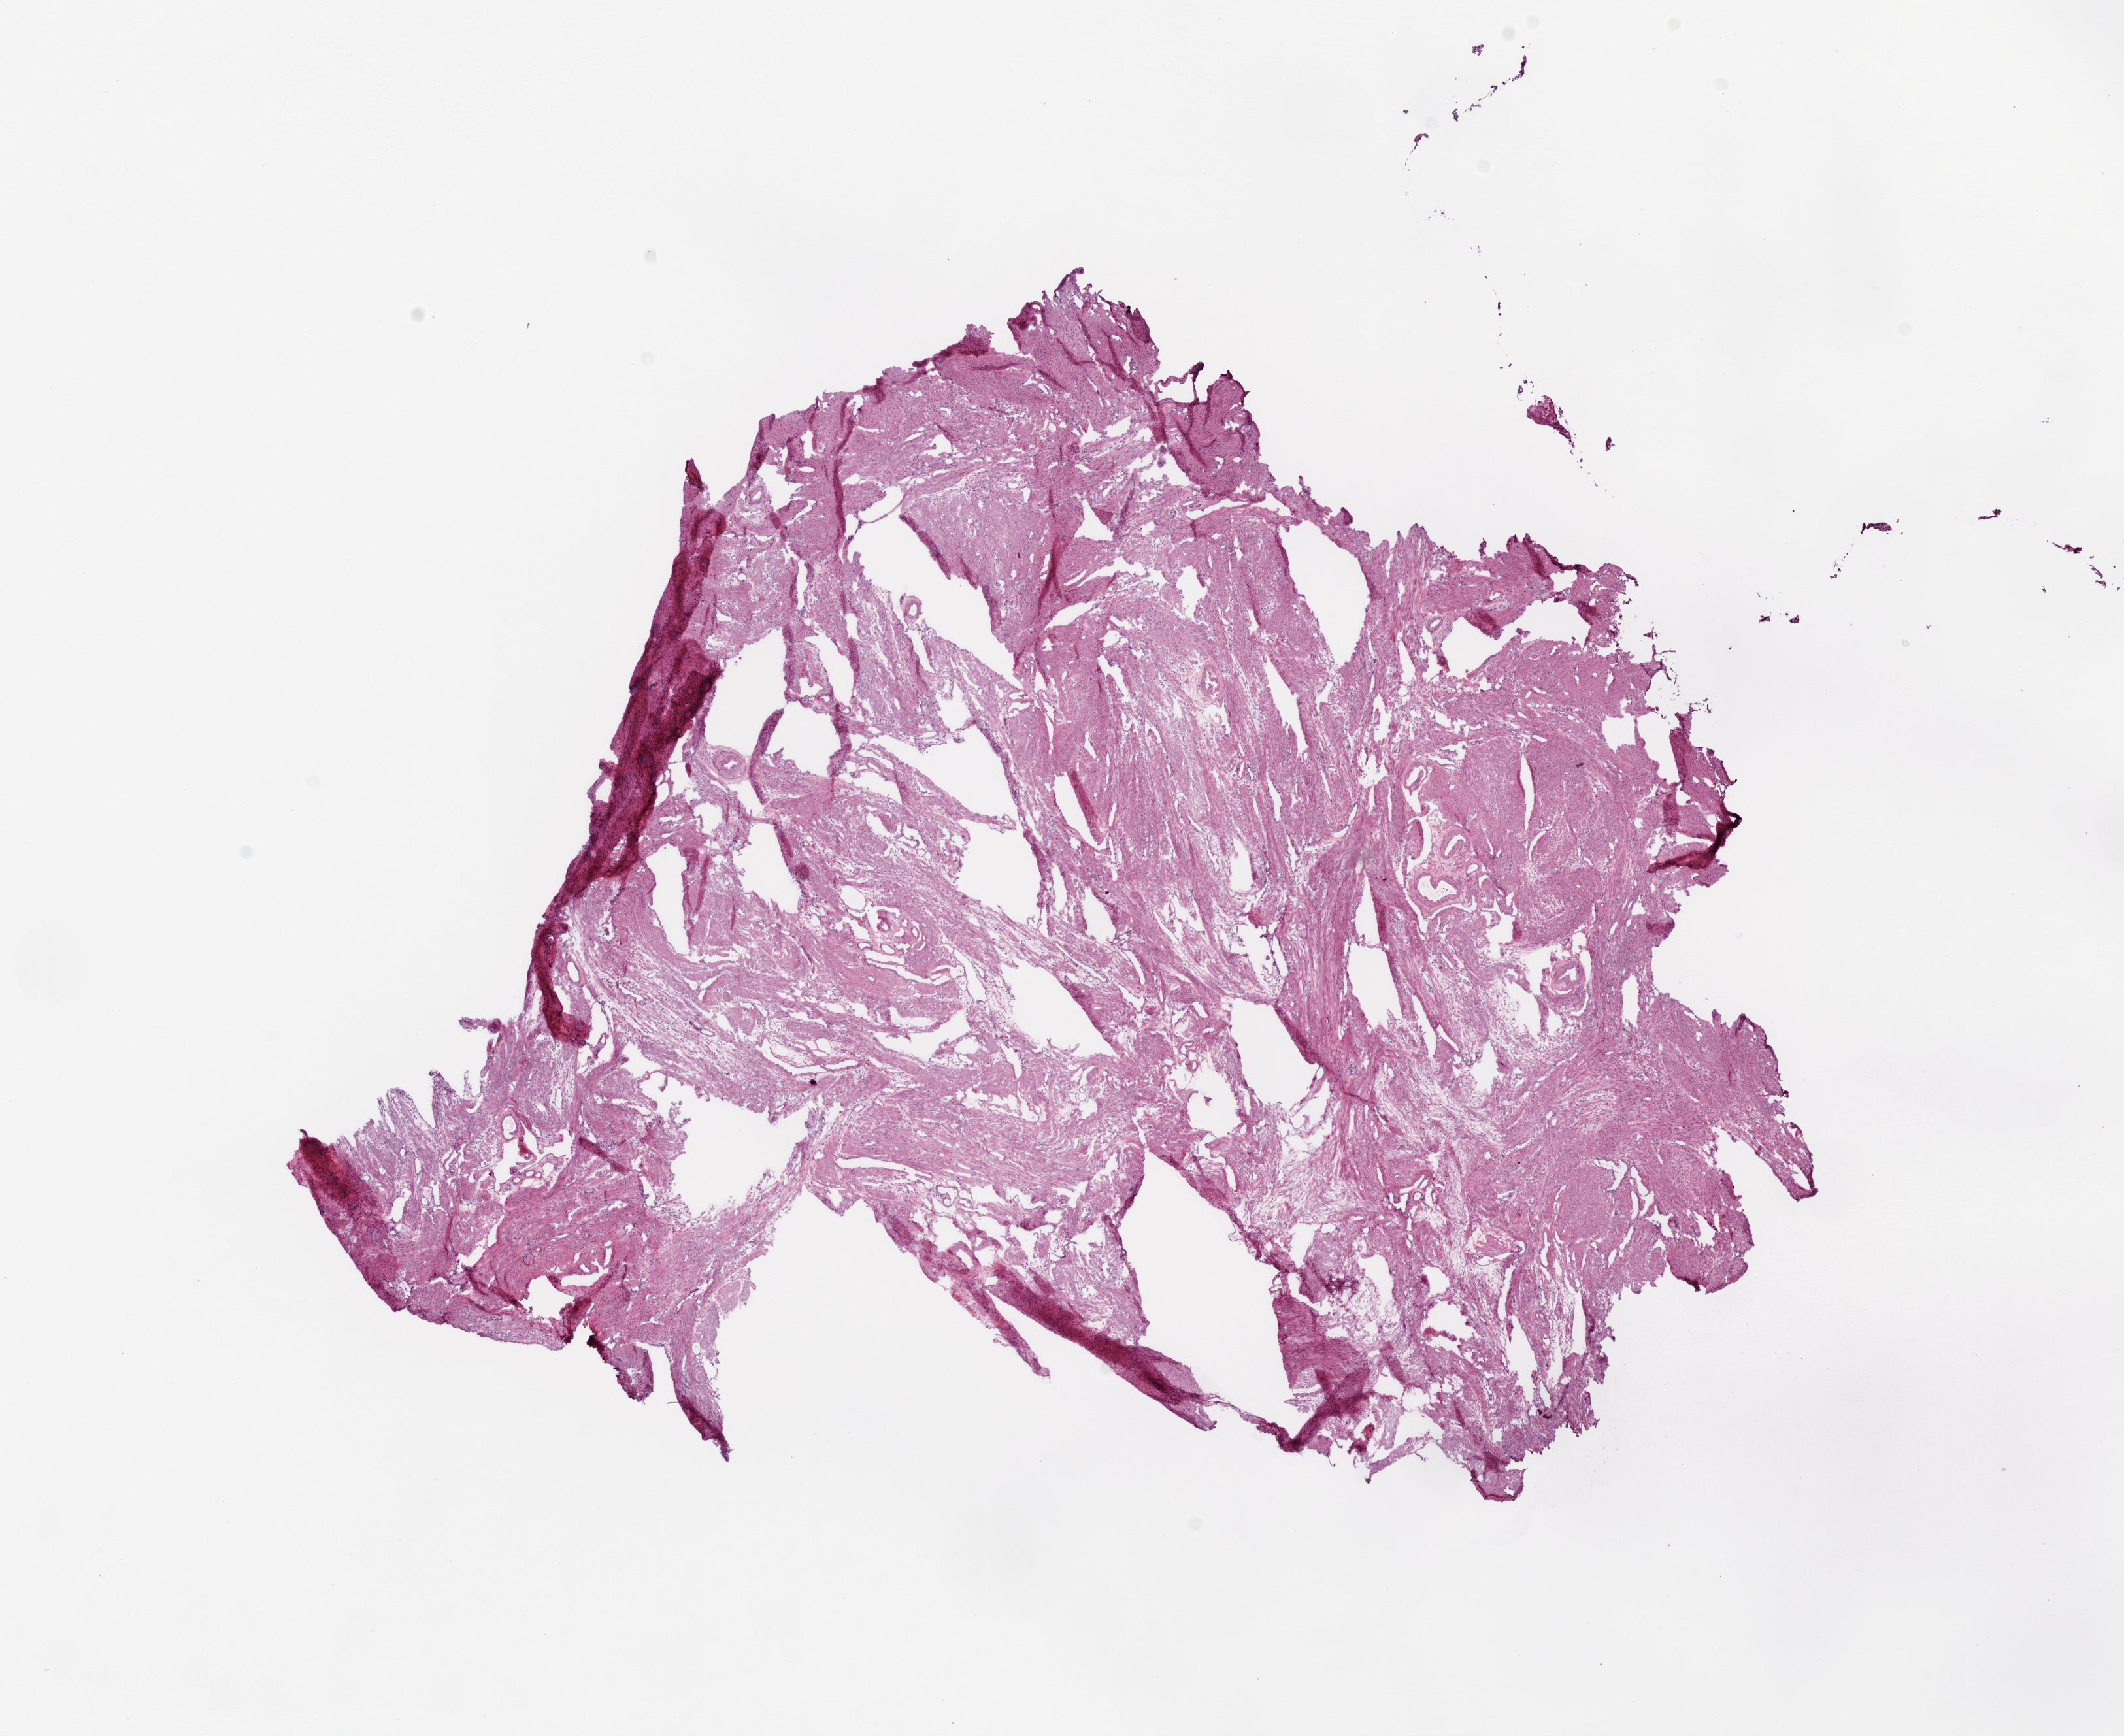
Digitized Hematoxylin and eosin (H&E) stained tissue section (whole slide) — whole scanned area (about 13.0 x 10.7 mm, slide scanned at 20x) shown as a low-resolution overview, frozen section from the bottom of the tissue portion, solid tissue normal (non-tumour tissue) sample from the ovary. Patient: female, age at initial diagnosis 44 years.
This section: solid tissue normal (non-tumour) sample from the same patient. Patient diagnosis: Serous cystadenocarcinoma, NOS.